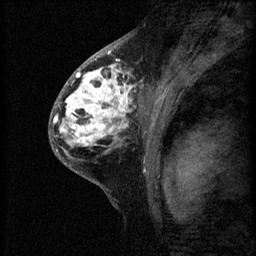
Breast MRI (dynamic contrast-enhanced), one sagittal slice; 3 images stored at this slice position (order not interpretable as contrast timing); 1.5 T; TE 4.2 ms, TR 8.2 ms; 2 mm slice thickness; 256 × 256 image matrix, field of view 180 × 180 mm. Patient: female, 41 years.
Structures marked on this image (semi-automatic segmentation, software-assisted and operator-edited):
- analysis volume of interest (the breast-tissue region the enhancement analysis was run in; not a lesion): bounding box (x1, y1, x2, y2) in pixels: (53, 62, 160, 175)
- tumour enhancement mask (voxels above the 70 % enhancement threshold inside the analysis volume of interest): (53, 64, 136, 151)